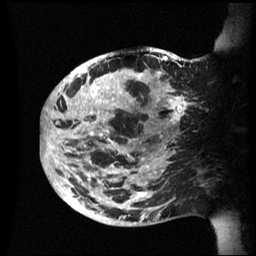
Breast MRI (dynamic contrast-enhanced), one sagittal slice; slice 21 of 60 in the series (ordered by position); dynamic contrast-enhanced series, image 2 of 3 at this slice position (ordered by acquisition); 1.5 T; TE 4.2 ms, TR 8.4 ms; 2.4 mm slice thickness; 256 × 256 image matrix. Female patient, age 48 years.
Annotated regions visible in this slice (semi-automatic segmentation, software-assisted and operator-edited):
- analysis volume of interest (the breast-tissue region the enhancement analysis was run in; not a lesion): box from (x=42, y=47) to (x=202, y=226) px
- tumour enhancement mask (voxels above the 70 % enhancement threshold inside the analysis volume of interest): (x=42, y=56)–(x=194, y=224)